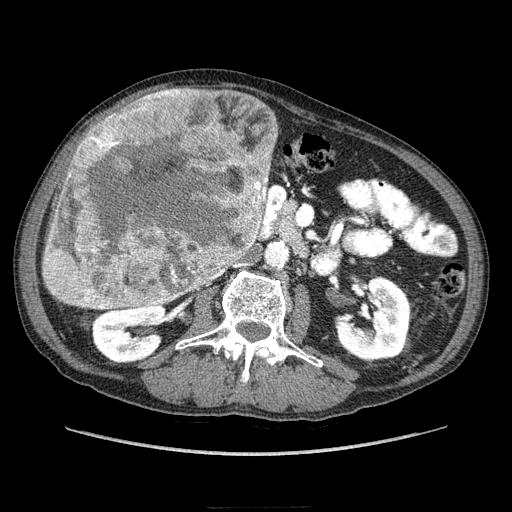
Contrast-enhanced abdominal CT (liver protocol), one axial slice. Slice 91 of 218 in the series (ordered by position). 100 kVp. Soft-tissue window (W 400 / L 40 HU). 512 × 512 image matrix, field of view 380 × 380 mm. From the clinical record (not read from this slice): diagnosis: hepatocellular carcinoma (patient treated with transarterial chemoembolisation; whether this scan precedes or follows treatment is not stated here); TNM stage (as recorded): Stage-IIIA; Child-Pugh class: A; tumour differentiation: well differentiated.
Outlined on this slice (semi-automatic segmentation, software-assisted and operator-edited):
- liver parenchyma outside the tumour (the mass and vessels are separate outlines, so this box may not span the whole liver): bounding box [x1, y1, x2, y2] px = [103, 110, 278, 253]
- mass: [40, 88, 275, 312]